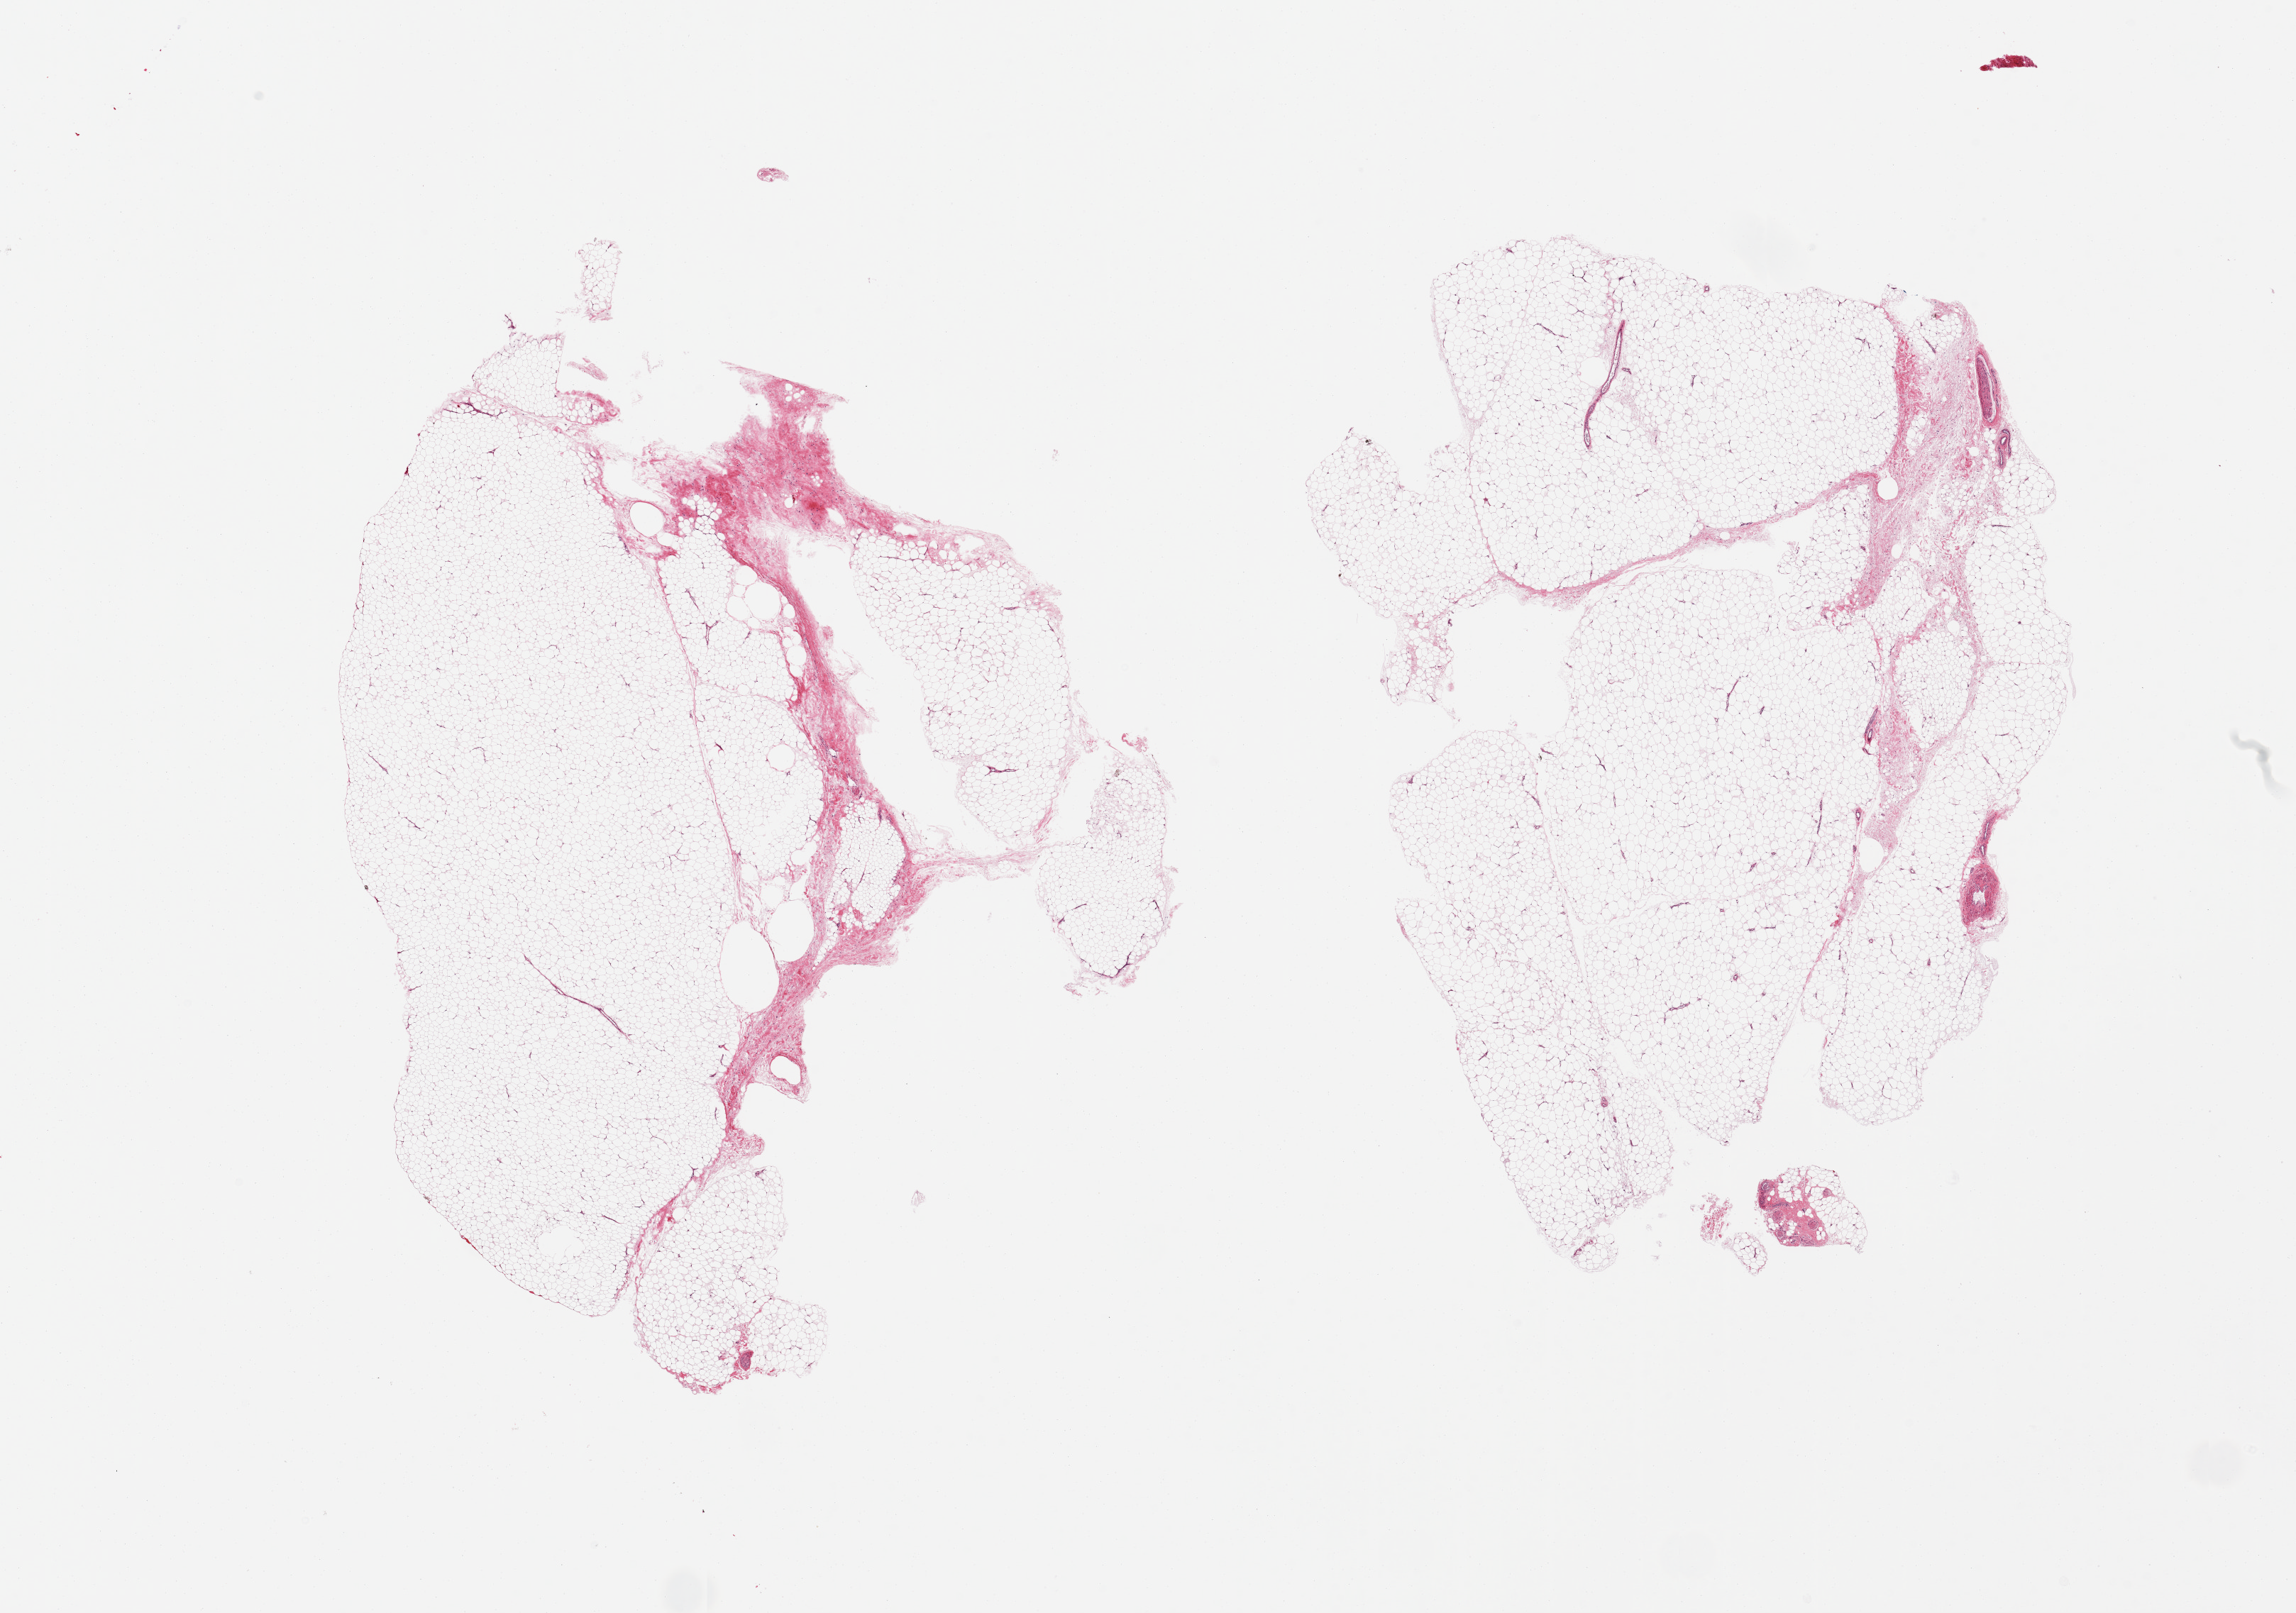
Haematoxylin and eosin whole-slide image, brightfield — whole scanned area (about 25.6 x 18.0 mm) shown as a low-resolution overview. PAXgene-fixed paraffin-embedded (PFPE) section. Target tissue: adipose tissue. Donor tissue sample. Male donor.
Reviewer comment on this tissue sample: 2 pieces, fascia is ~10-20%.